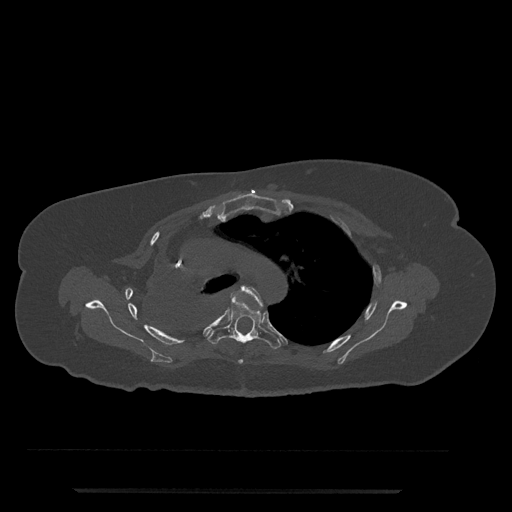
CT including the spine, one axial slice; position 555 of 797 along the scan axis; 120 kVp; bone window (W 1800 / L 400 HU); 0.5 mm slice thickness; 512 × 512 image matrix, field of view 440 × 440 mm. Patient: female, 51 years. From the clinical record (not read from this slice): primary cancer: neuro.
Outlined on this slice (semi-automatic segmentation, software-assisted and operator-edited):
- T4 vertebra: box from (x=238, y=285) to (x=263, y=364) px
- T5 vertebra: (x=207, y=296)–(x=281, y=349)